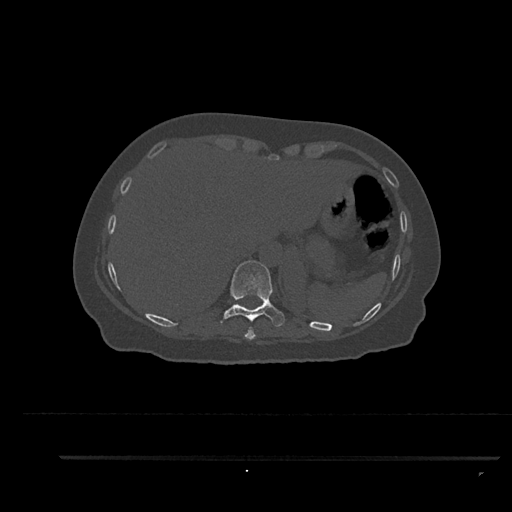
CT including the spine, one axial slice. Position 367 of 797 along the scan axis. Reconstruction kernel Br40s/3. 120 kVp. Bone window (W 1800 / L 400 HU). 0.5 mm slice thickness. 512 × 512 image matrix, field of view 408 × 408 mm. Patient: female, 44 years. Case-level facts recorded for this patient, not image findings: primary cancer: renal; vertebrae with lytic lesions (as recorded): L1.
Annotated regions visible in this slice (semi-automatically segmented with operator editing):
- T10 vertebra: bounding box (x1, y1, x2, y2) in pixels: (220, 260, 285, 332)
- T9 vertebra: (244, 328, 256, 340)